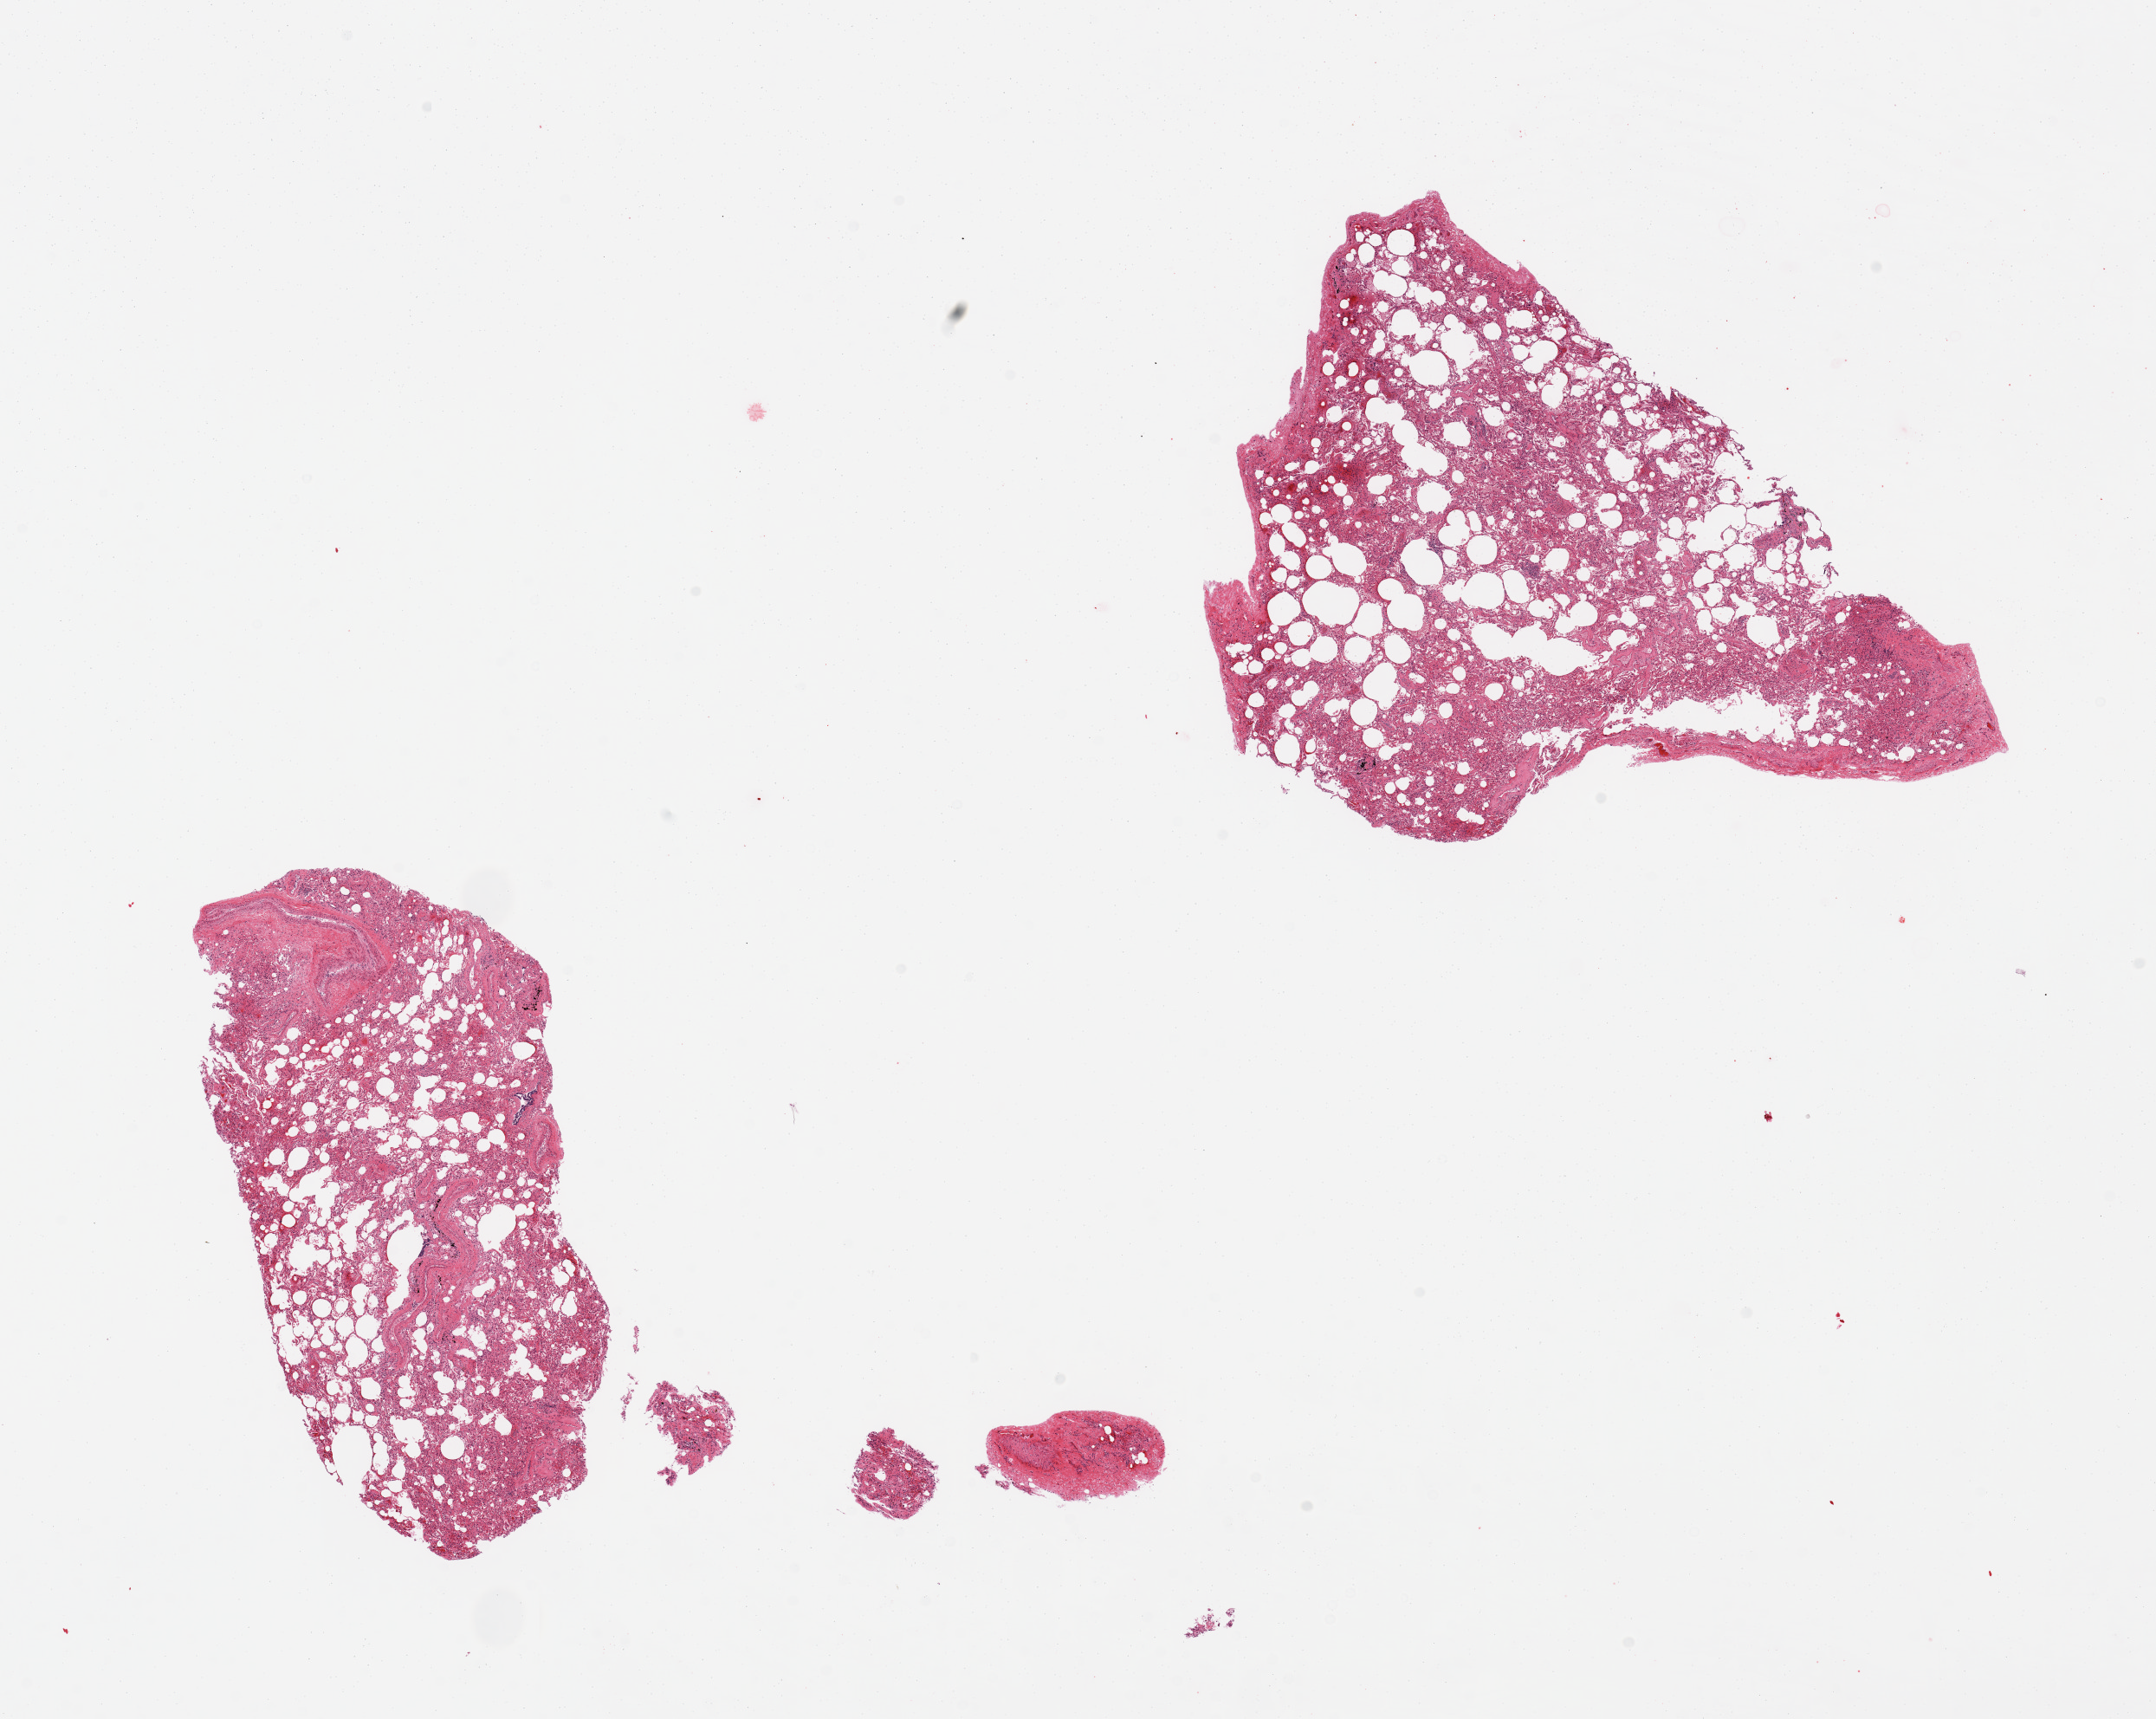
Digitized H&E-stained section, brightfield — shown as a low-resolution overview of the whole scanned area (about 19.7 x 15.7 mm, acquisition: 20x scan), PAXgene-fixed, paraffin-embedded tissue, sampled site (target tissue): lung, donor tissue sample. Donor sex: male.
• review note (as recorded): 2 pieces